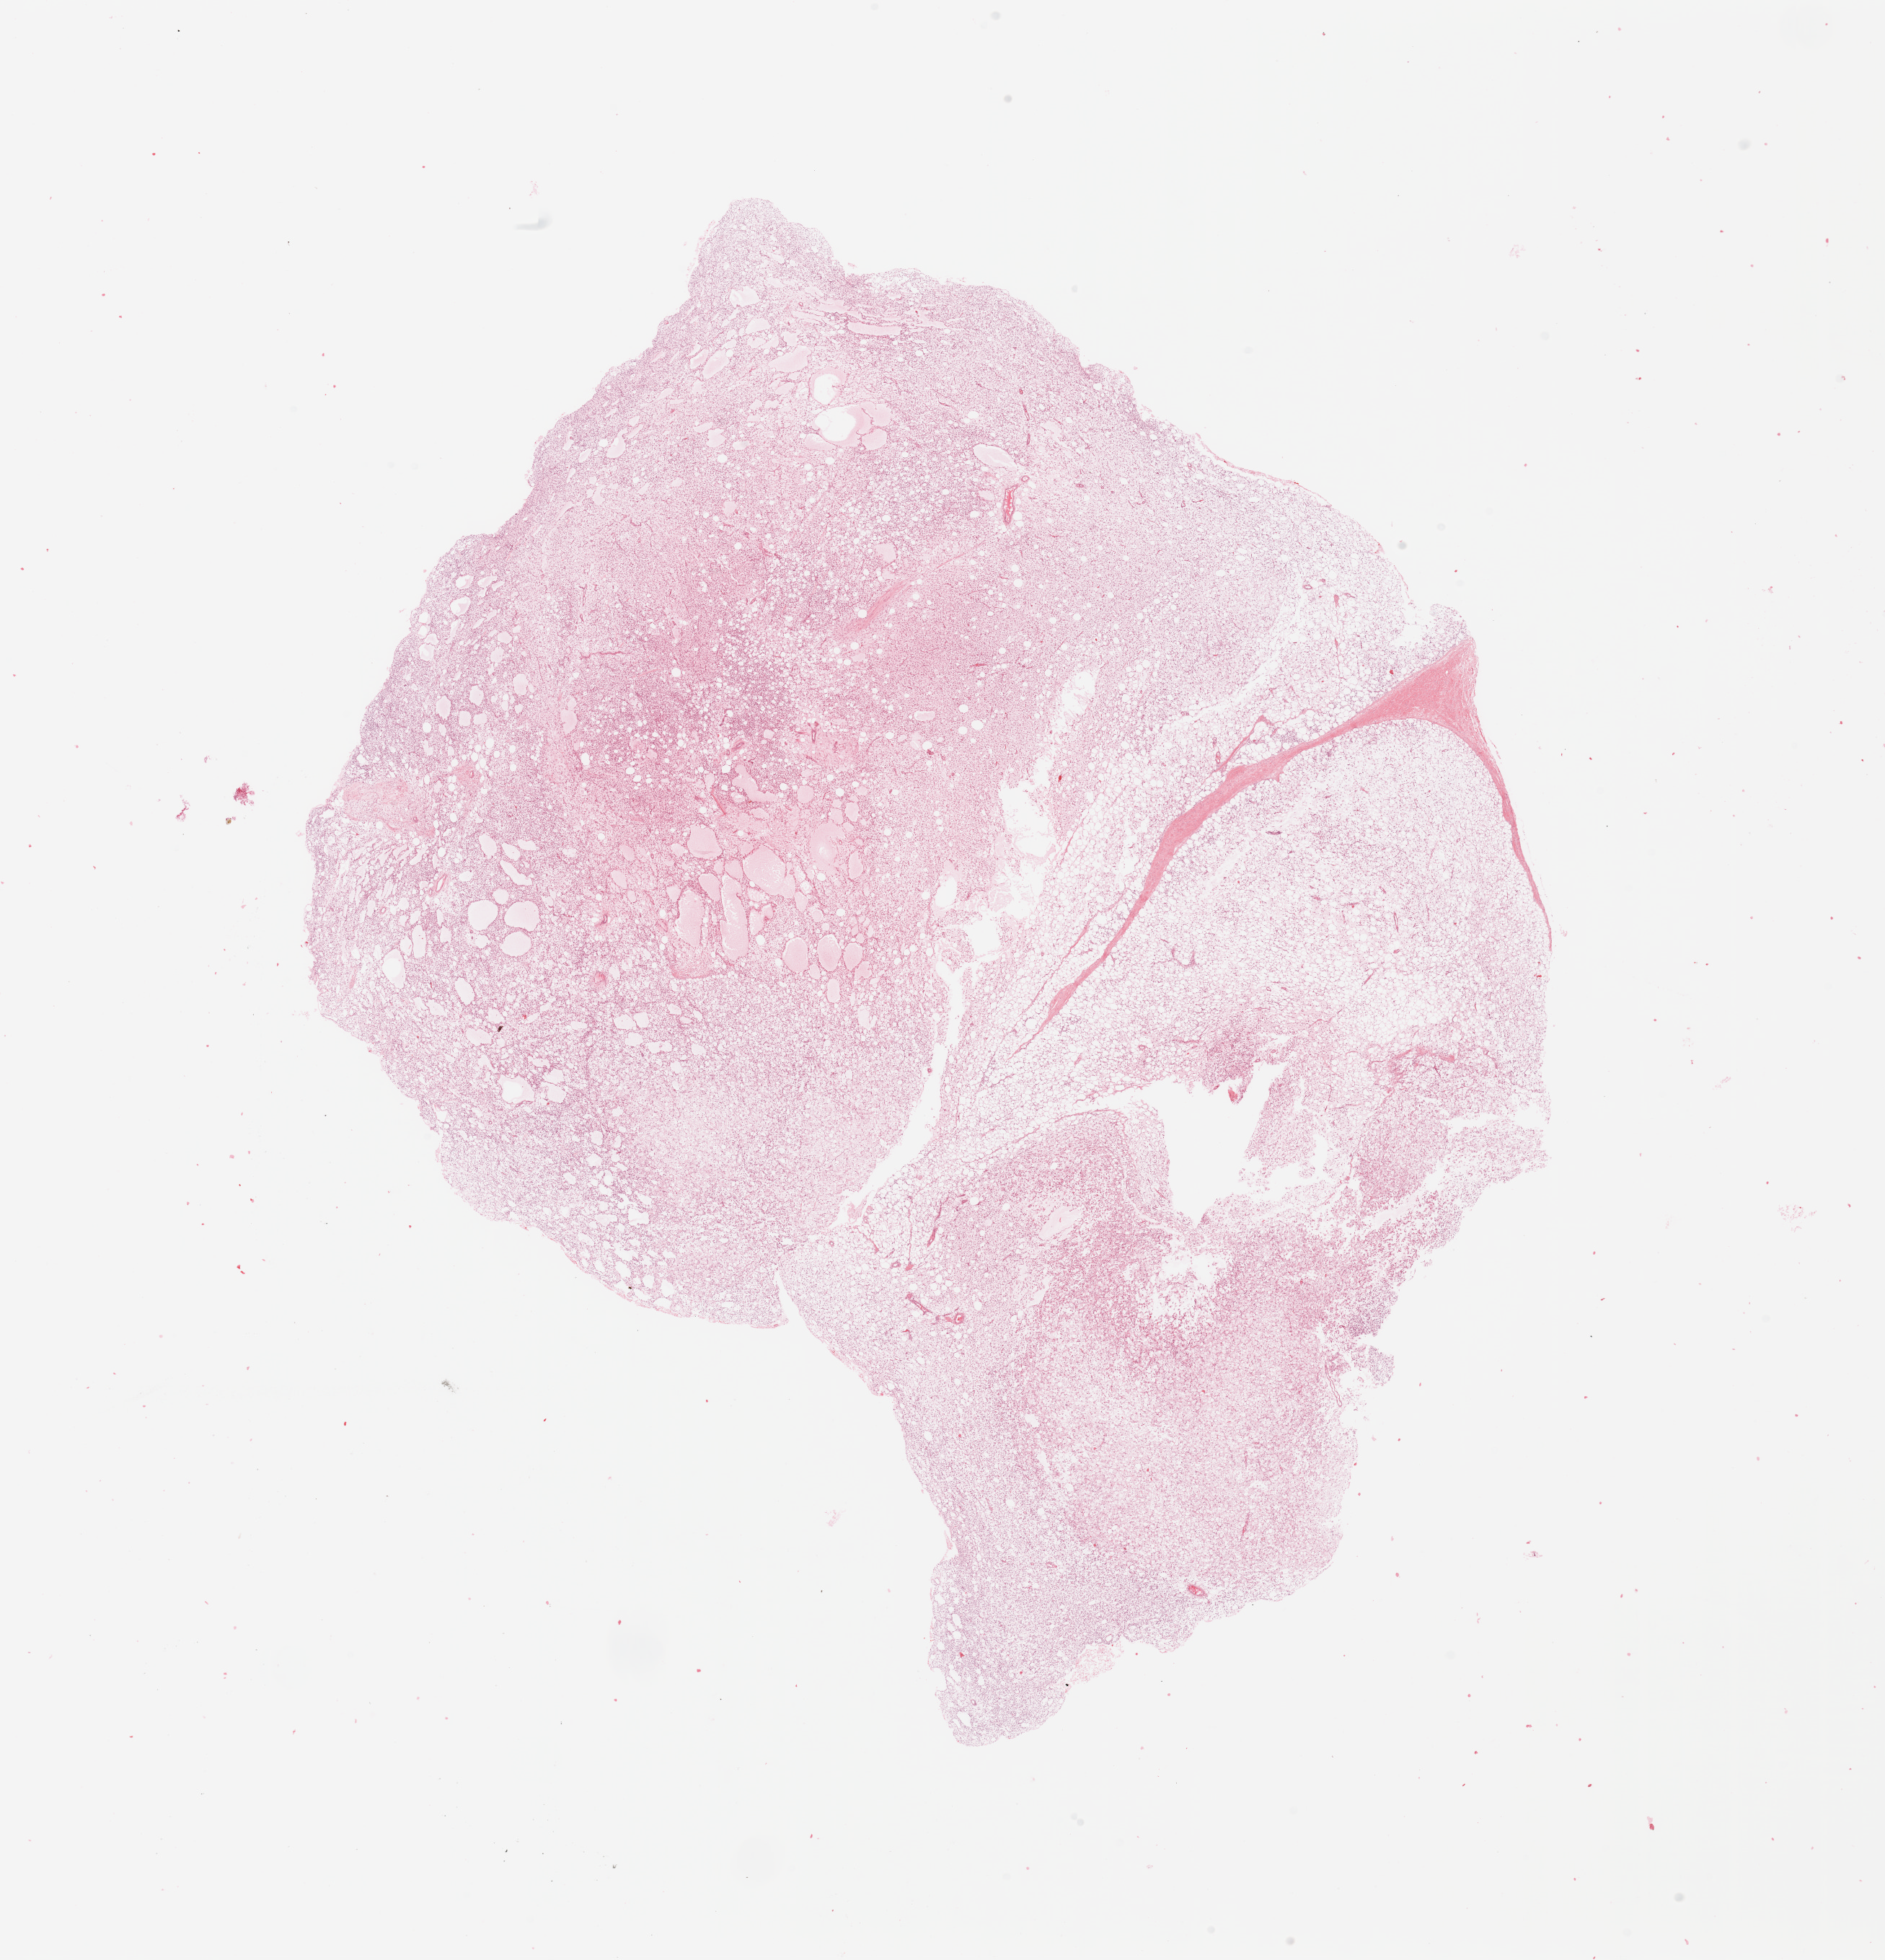
Digitized H&E-stained tissue section (whole slide), a low-resolution overview of the entire scanned area, about 20.7 x 21.5 mm (slide scanned at 20x); tumour tissue sample. Patient: female, age 32 years.
* patient diagnosis (cohort enrolment): sarcoma (site not recorded at cohort level)
* primary tumour site (as recorded): lower extremity